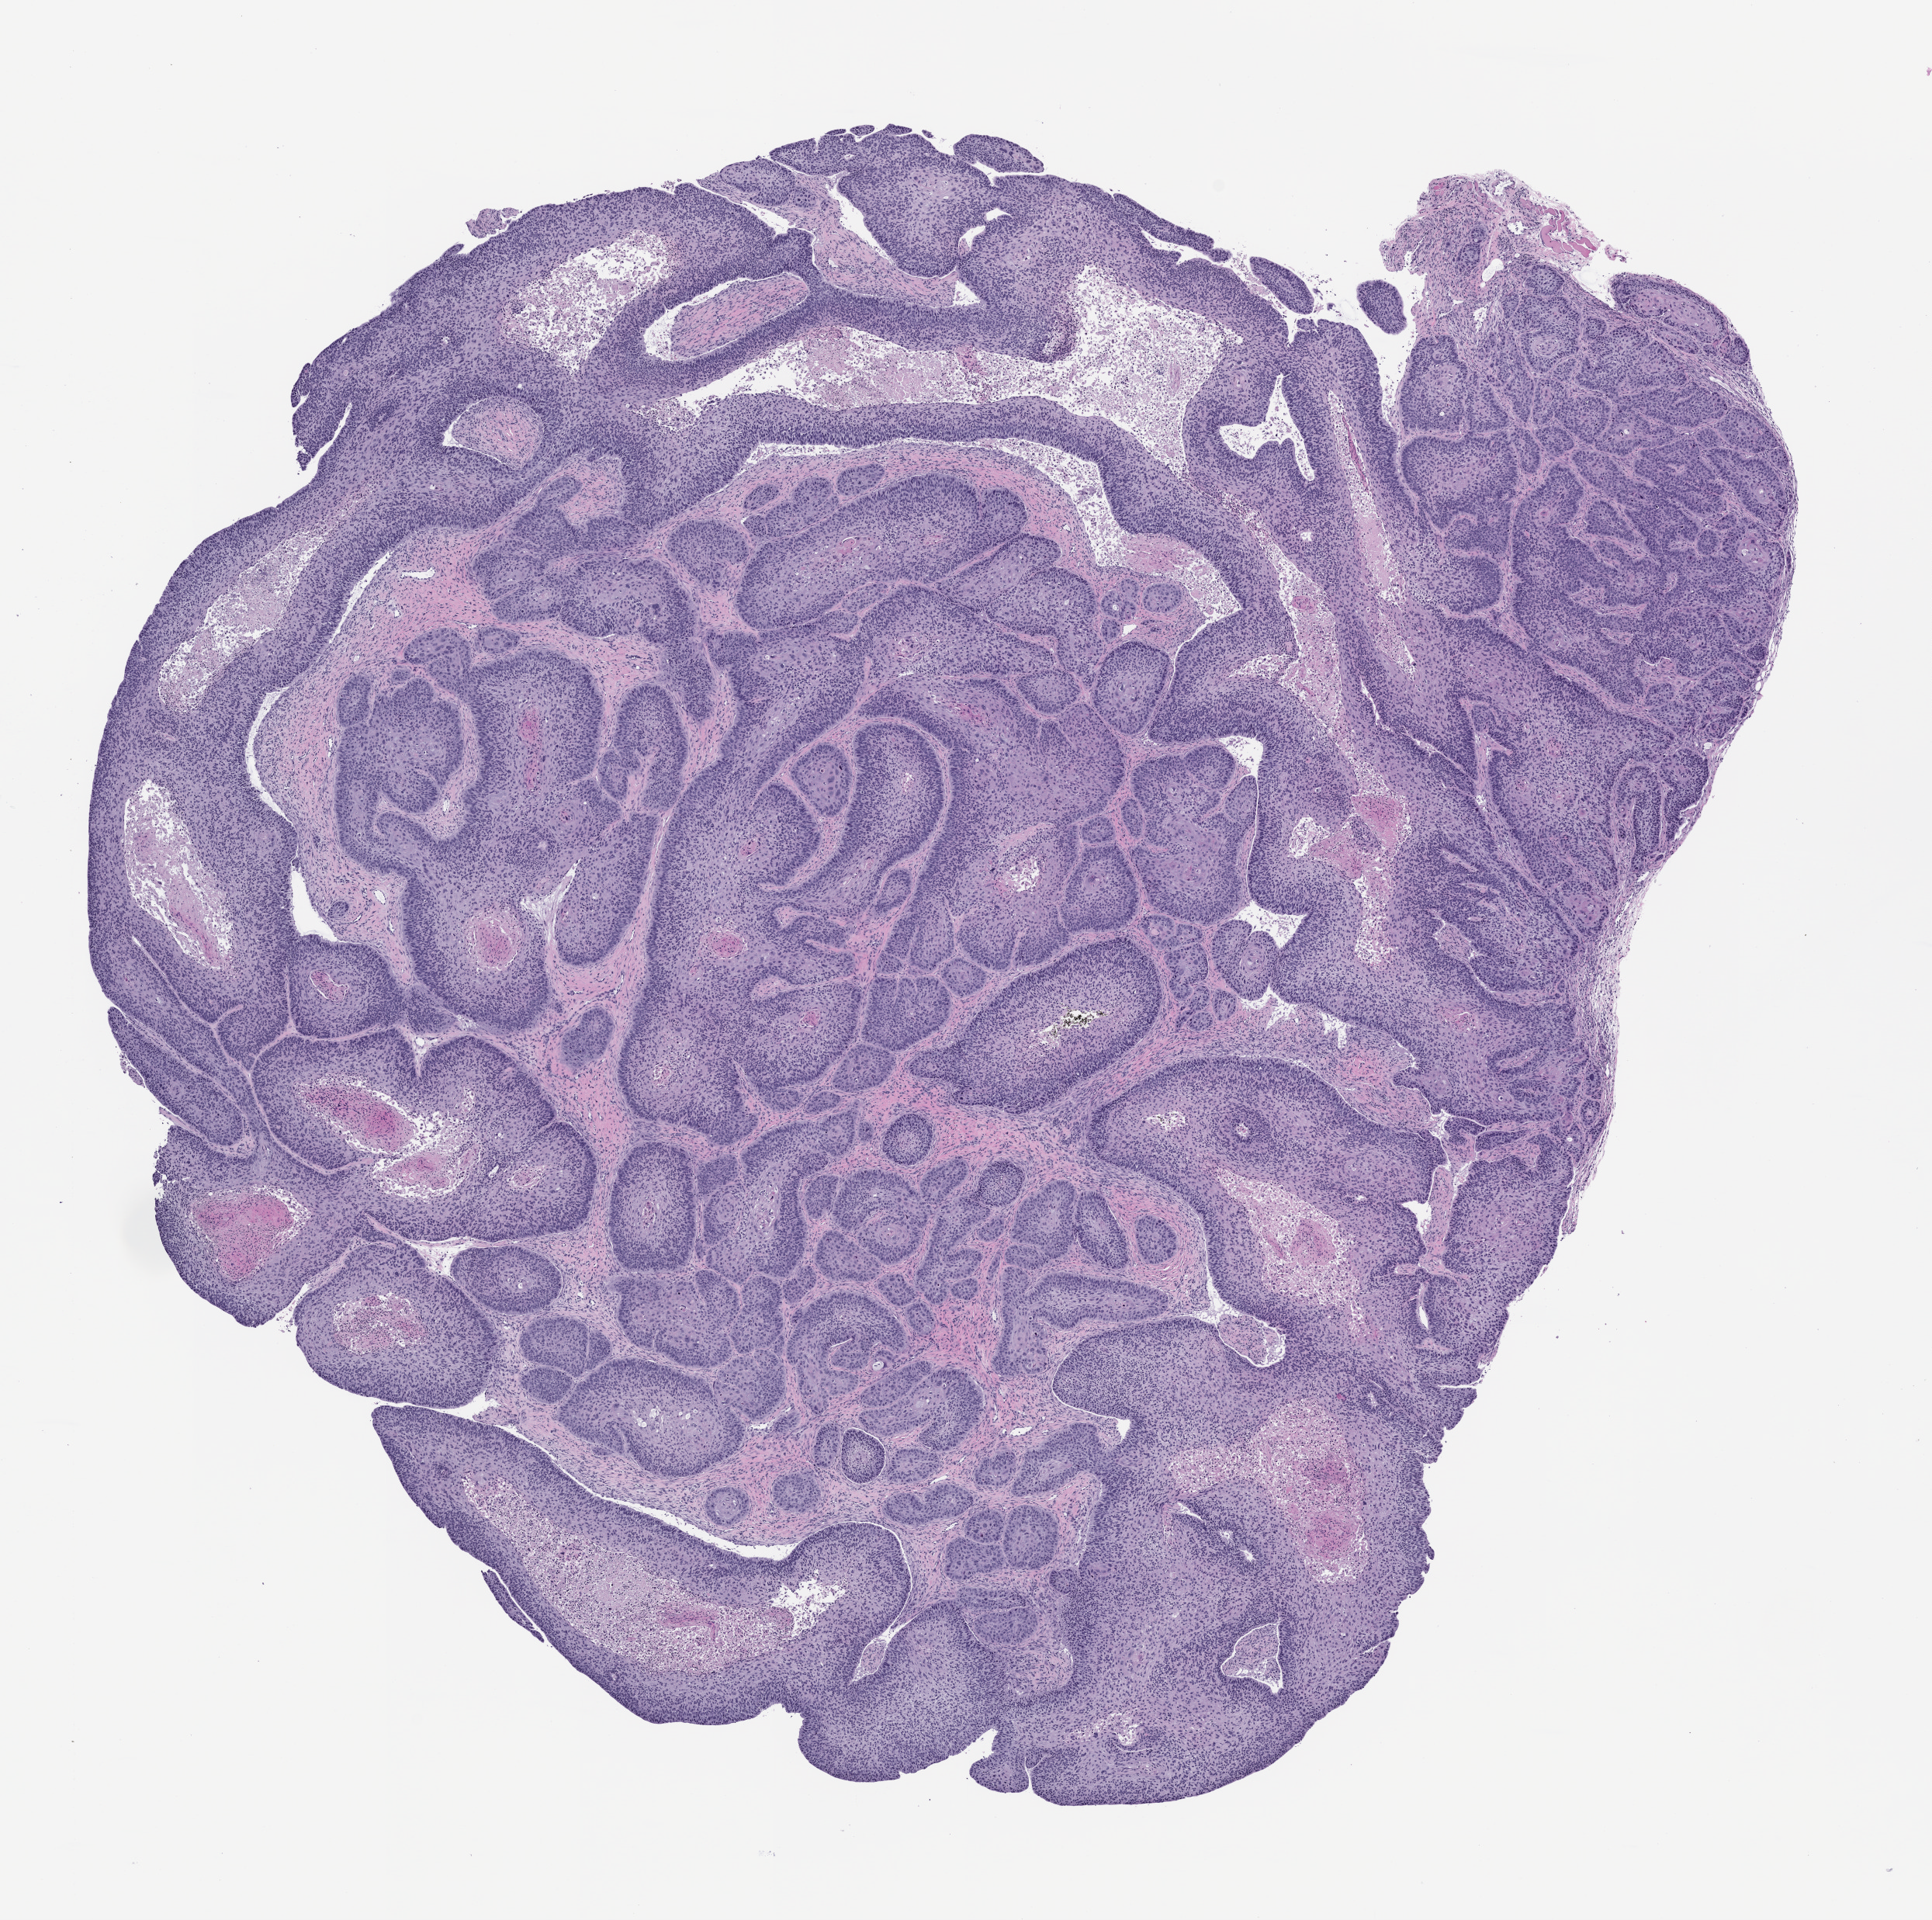
Whole-slide image, H&E: patient-derived xenograft (human tumor grown in a mouse), passage 2 — a low-resolution overview of the entire scanned area, about 10.0 x 9.9 mm; FFPE section; originating tumor site category: head and neck.
Originating patient diagnosis: Head and Neck Squamous Cell Carcinoma.